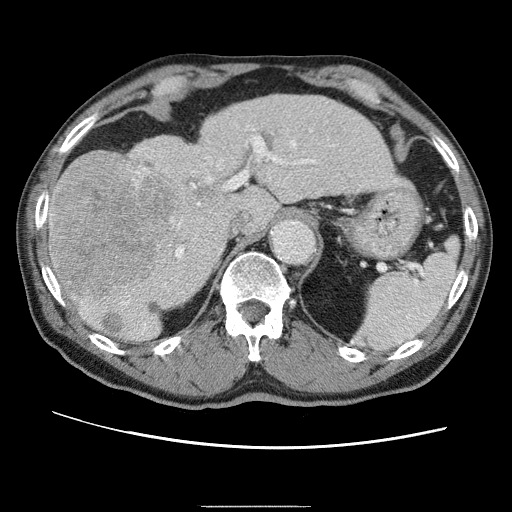
Contrast-enhanced abdominal CT (liver protocol), one axial slice. Slice 39 of 75 in the series (ordered by position). Reconstruction kernel STANDARD. One of 2 acquisitions stored at this slice position. Soft-tissue window (W 400 / L 40 HU). 2.5 mm slice thickness. 512 × 512 image matrix, field of view 360 × 360 mm. From the clinical record (not read from this slice): diagnosis: hepatocellular carcinoma (patient treated with transarterial chemoembolisation; whether this scan precedes or follows treatment is not stated here); TNM stage (as recorded): Stage-II; Child-Pugh class: A; tumour differentiation: well differentiated; tumour nodularity: multinodular.
Outlined on this slice (semi-automatically segmented with operator editing):
- liver parenchyma outside the tumour (the mass and vessels are separate outlines, so this box may not span the whole liver): bounding box <48,94,402,340> (left, top, right, bottom; pixels)
- mass: <49,154,179,294>
- liver vessels: <80,128,348,316>